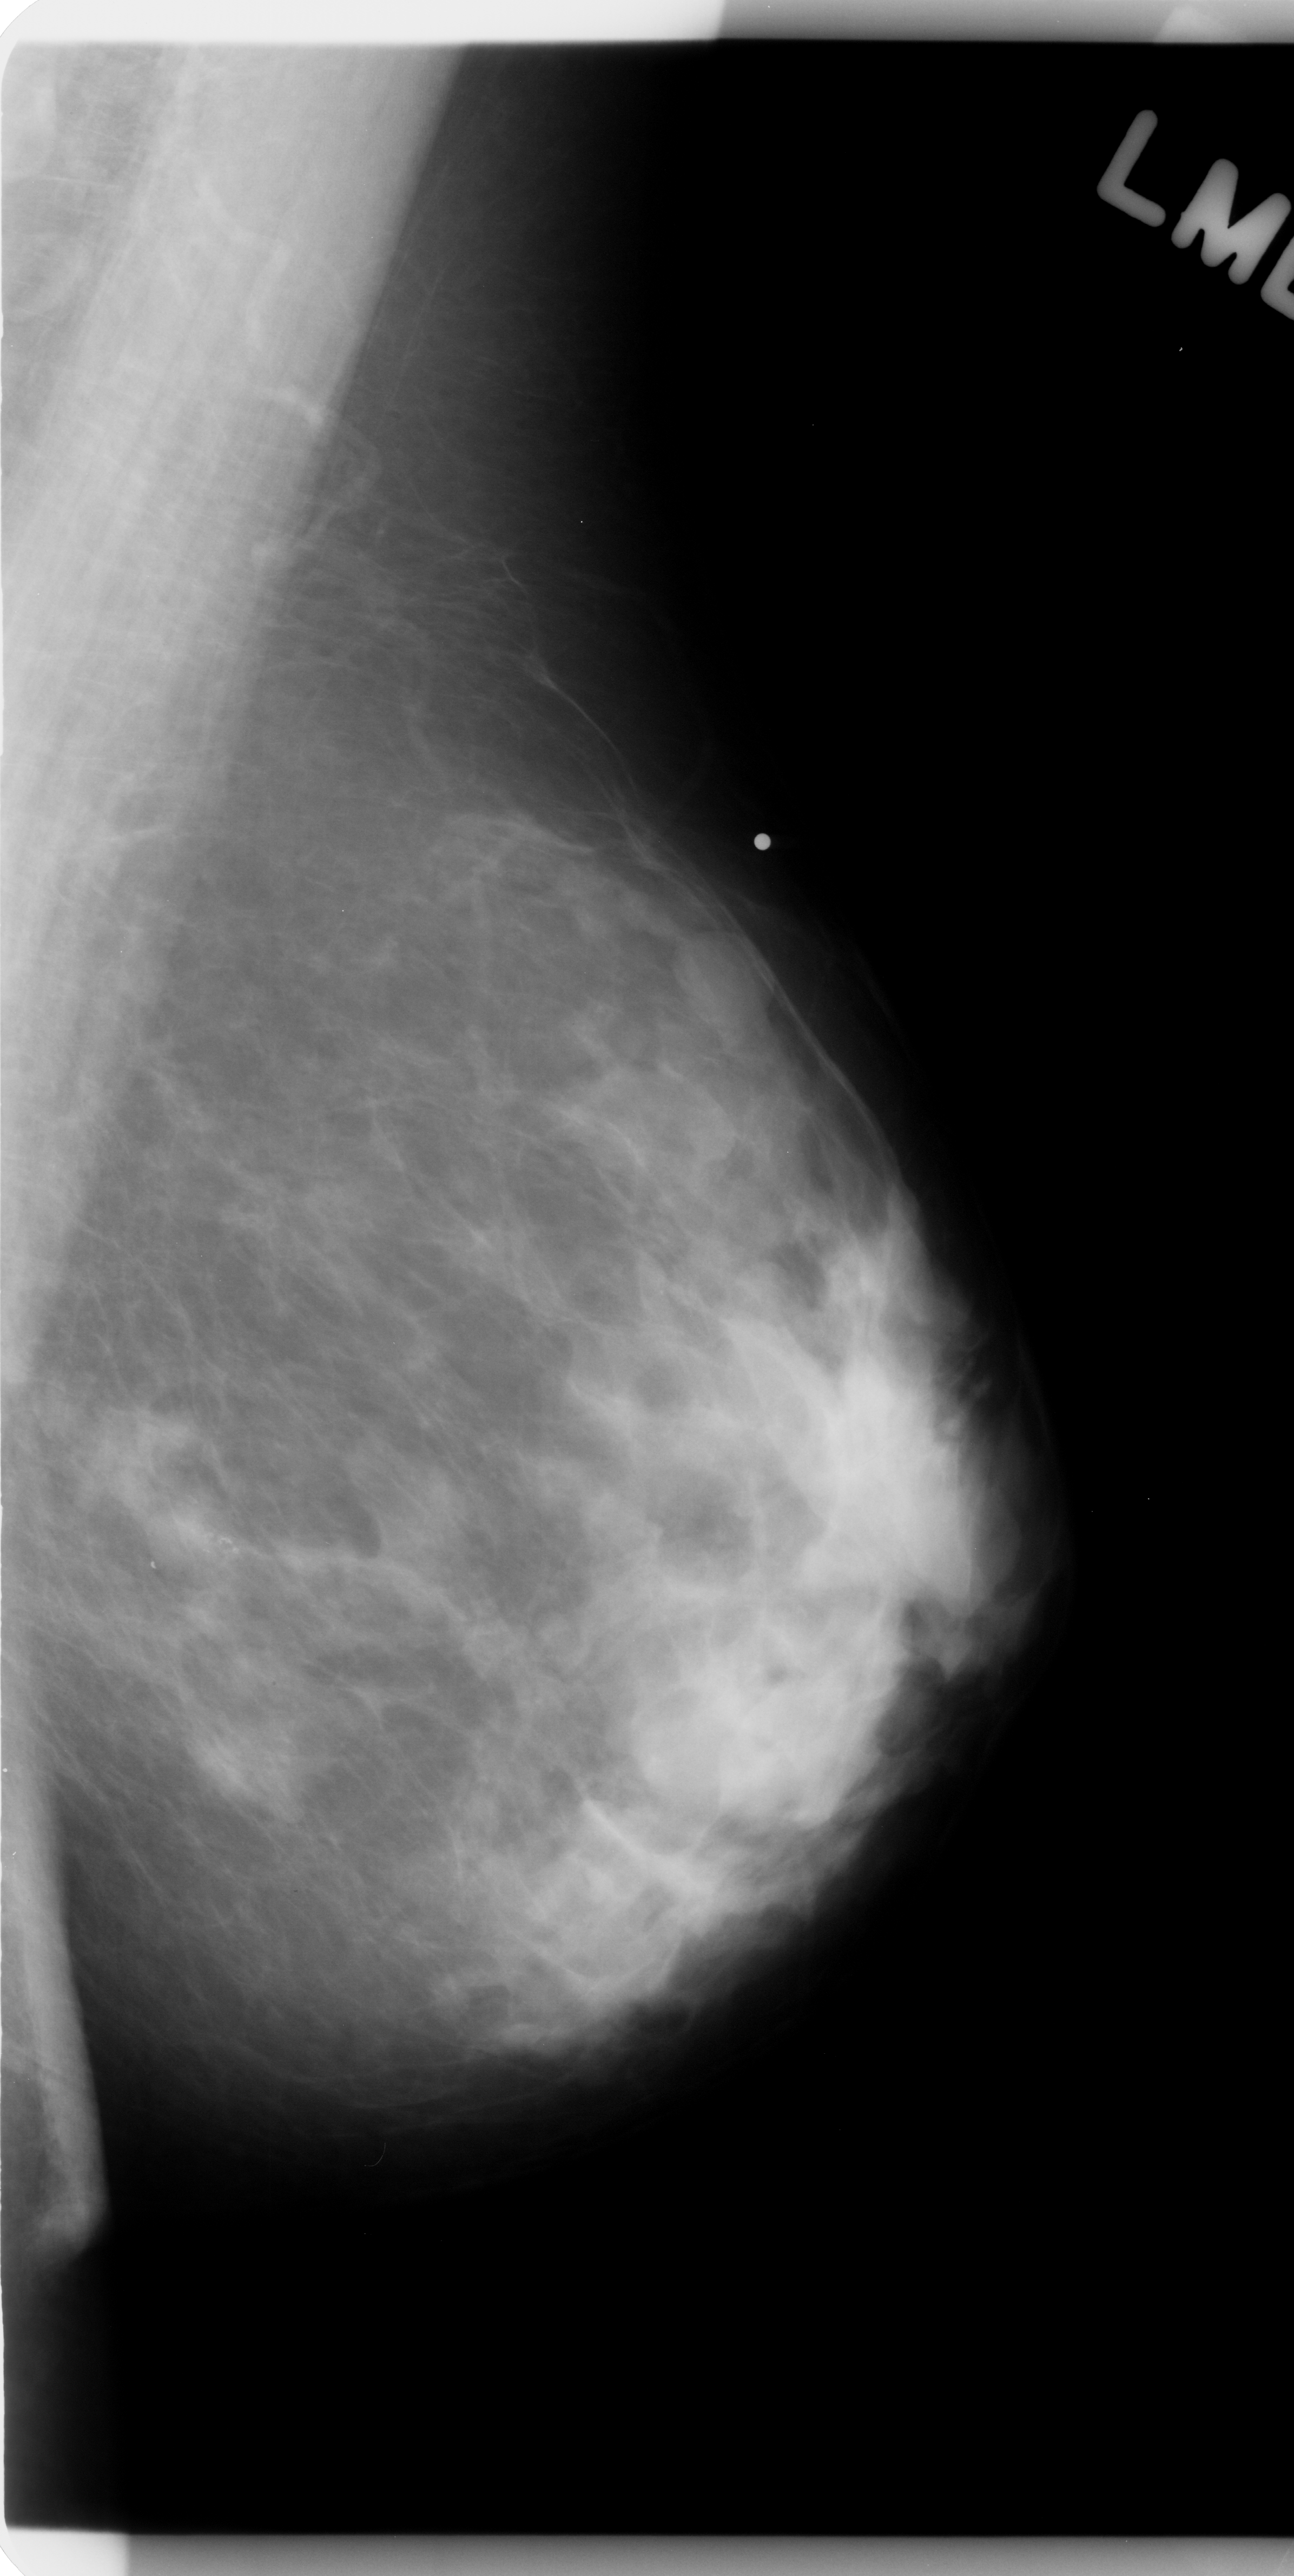
Digitized screen-film mammogram; left breast; mediolateral oblique (MLO) view; breast composition: heterogeneously dense (BI-RADS density category 3 of 4); 1294 × 2576 image matrix.
Expert-marked regions of interest on this film, with their recorded descriptors:
- calcifications, morphology amorphous, distribution clustered; BI-RADS assessment category 4; subtlety rating 3 on a 1 (subtle) to 5 (obvious) scale; pathology (as recorded): benign: bounding box <138,1459,300,1659> (left, top, right, bottom; pixels)